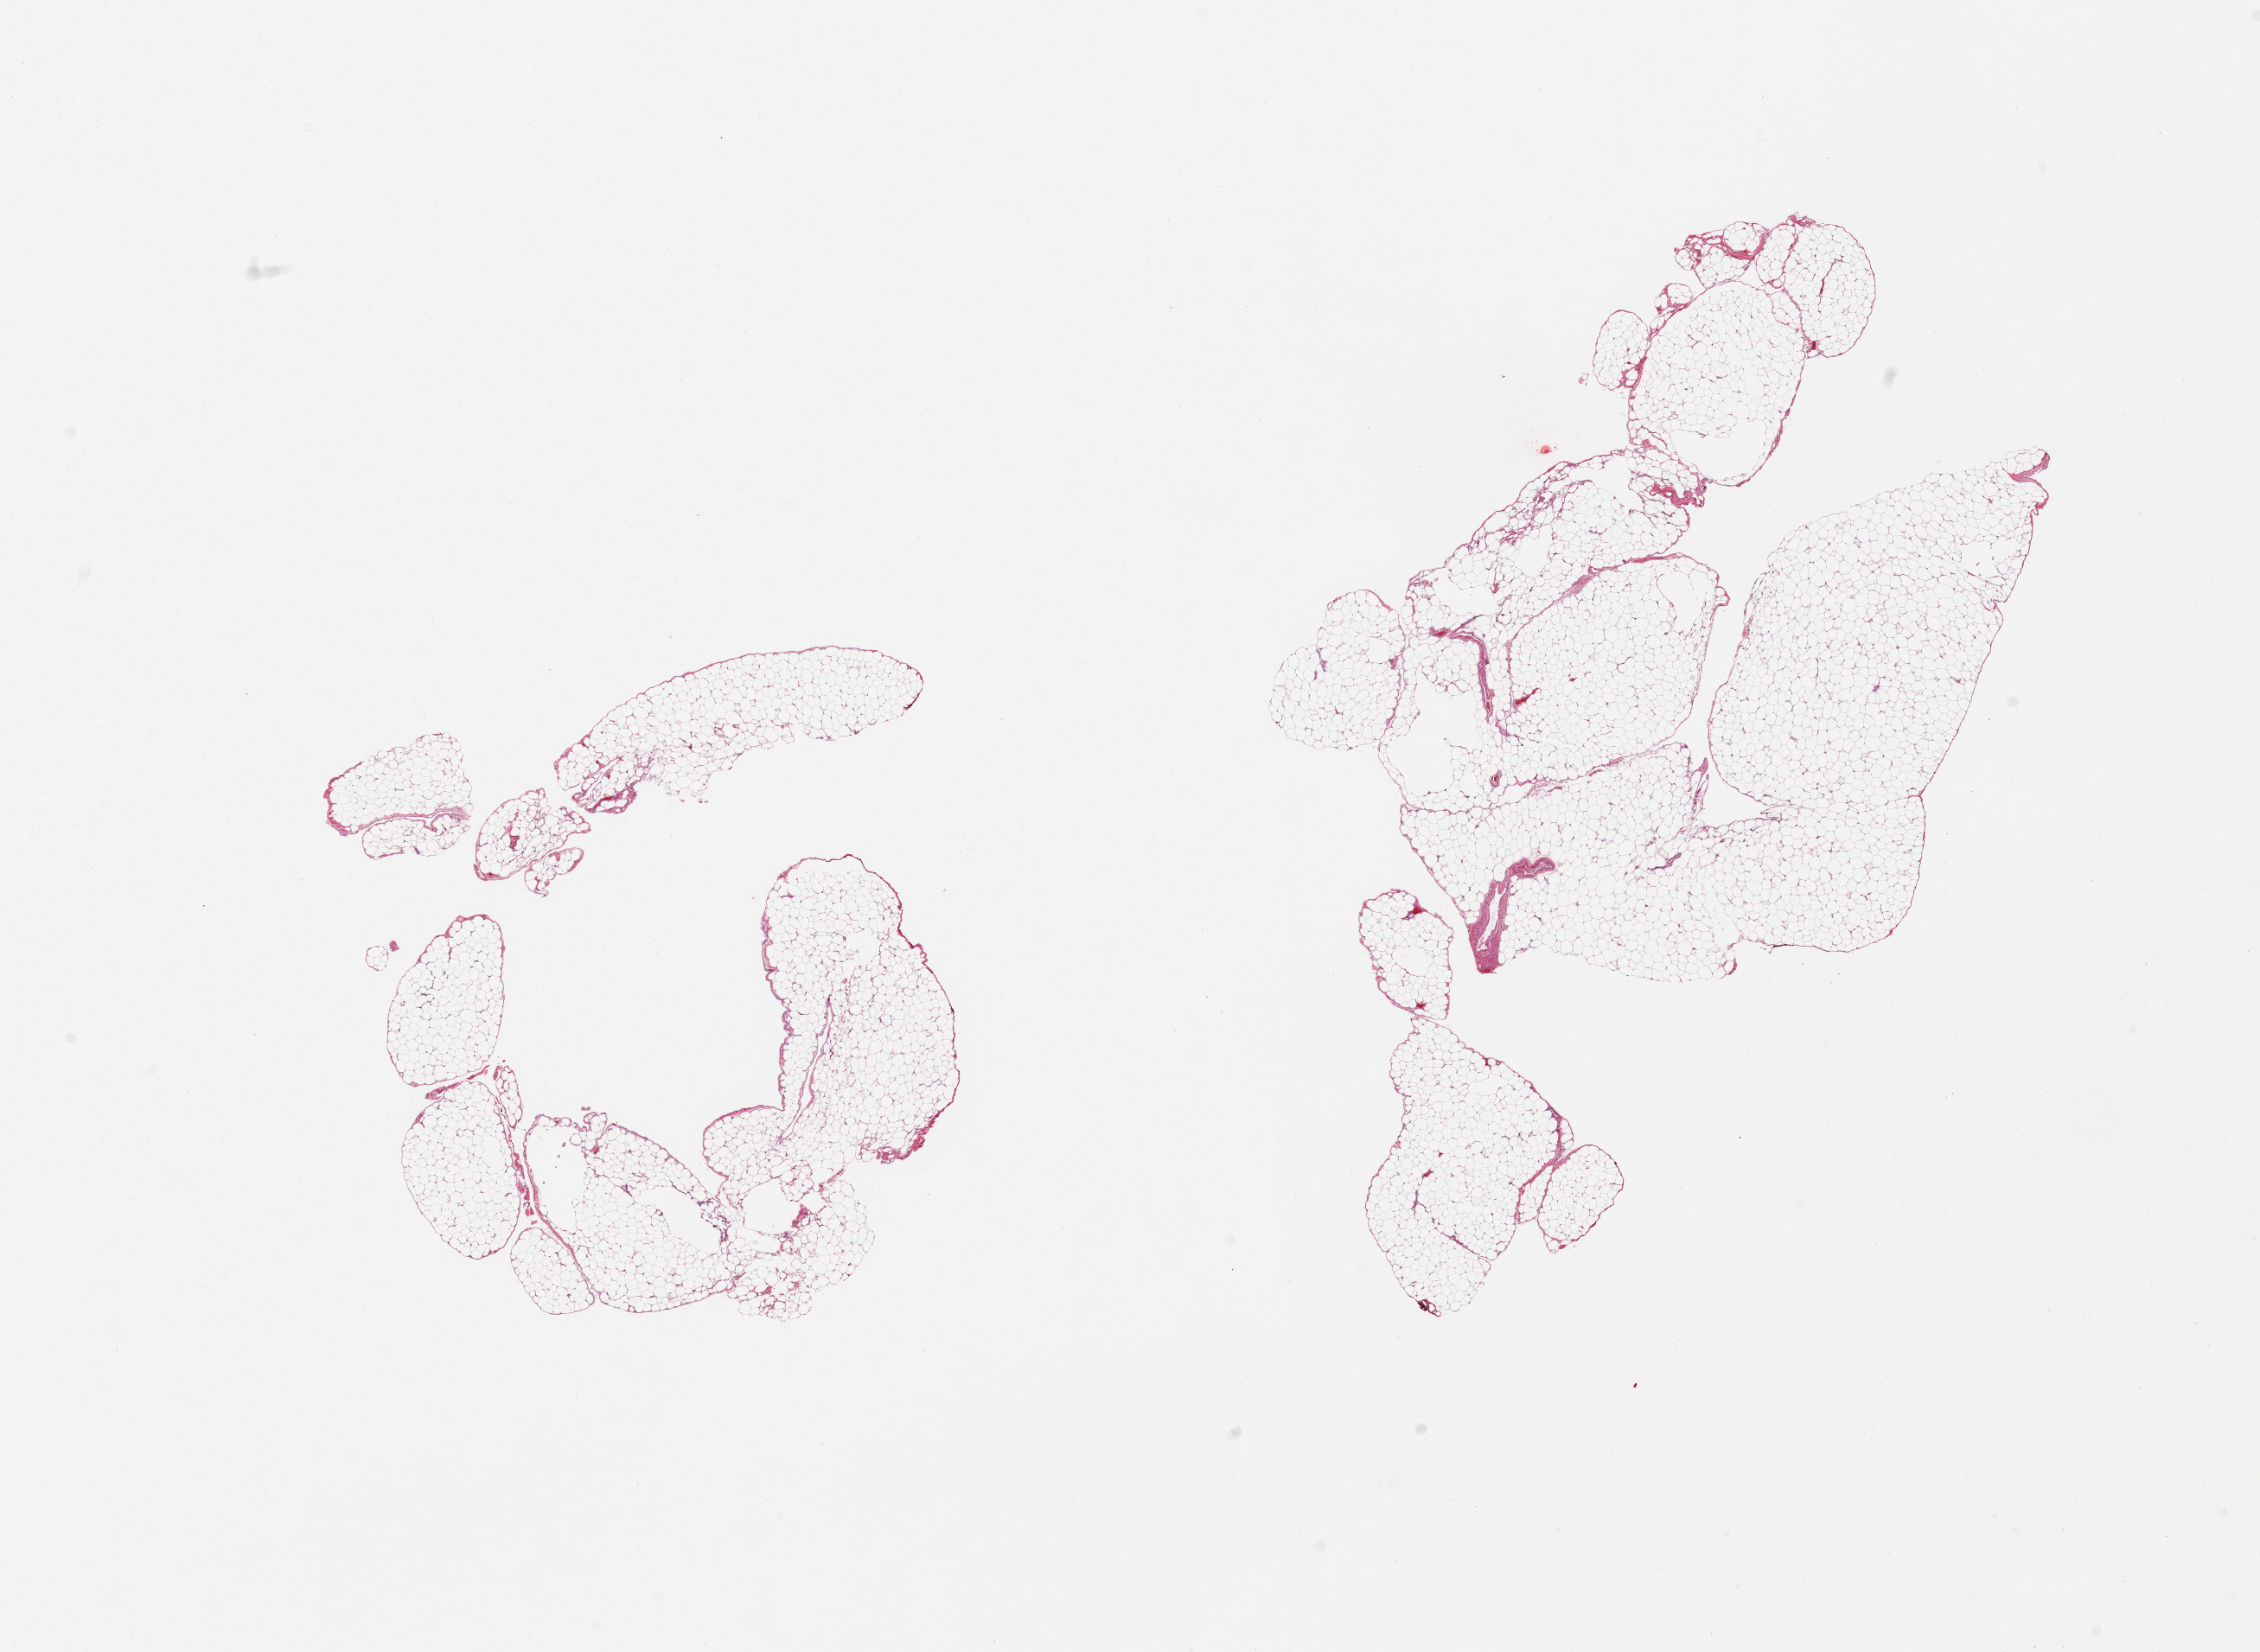
Haematoxylin and eosin whole-slide image, brightfield — whole scanned area (about 20.7 x 15.1 mm, slide scanned at 20x) shown as a low-resolution overview, PAXgene-fixed paraffin-embedded (PFPE) section, sampled site (target tissue): omentum, tissue donor sample. Donor: female.
Pathologist's review note for this sample: 2 pieces.